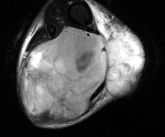
MRI of an extremity soft-tissue mass, one axial slice. T2-weighted fat-saturated. MR volume resampled by the dataset authors to the PET/CT grid (not the native acquisition matrix). 3.27 mm slice thickness. 165 × 137 image matrix. Male patient. From the clinical record (not read from this slice): histological type: liposarcoma - round cell; grade: high; site of the primary tumour: right calf.
Annotated regions visible in this slice (expert contour drawn on MRI and transferred to this co-registered scan by the dataset authors):
- gross tumour volume (mass): bounding box (x1, y1, x2, y2) in pixels: (19, 25, 143, 120)